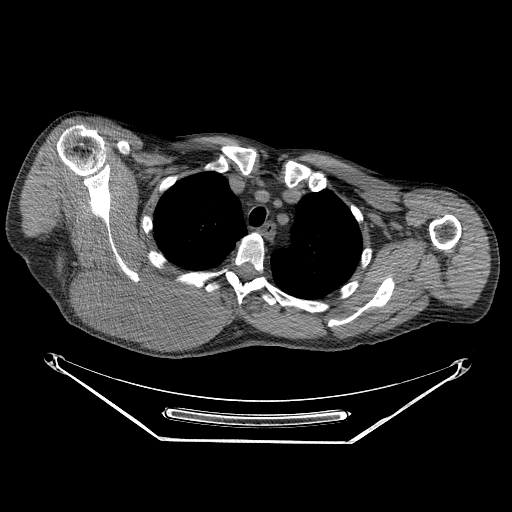
CT of an extremity soft-tissue mass (from a PET/CT study), one axial slice; slice 193 of 267 in the series (ordered by position); reconstruction kernel STANDARD; soft-tissue window (W 400 / L 40 HU); 3.75 mm slice thickness; 512 × 512 image matrix. Male patient. From the clinical record (not read from this slice): histological type: pleiomorphic spindle cell undifferentiated; grade: high; site of the primary tumour: right parascapusular.
Outlined on this slice (expert contour drawn on MRI and transferred to this co-registered scan by the dataset authors):
- gross tumour volume including surrounding oedema: bounding box <78,260,232,339> (left, top, right, bottom; pixels)
- gross tumour volume (mass): <78,260,213,336>